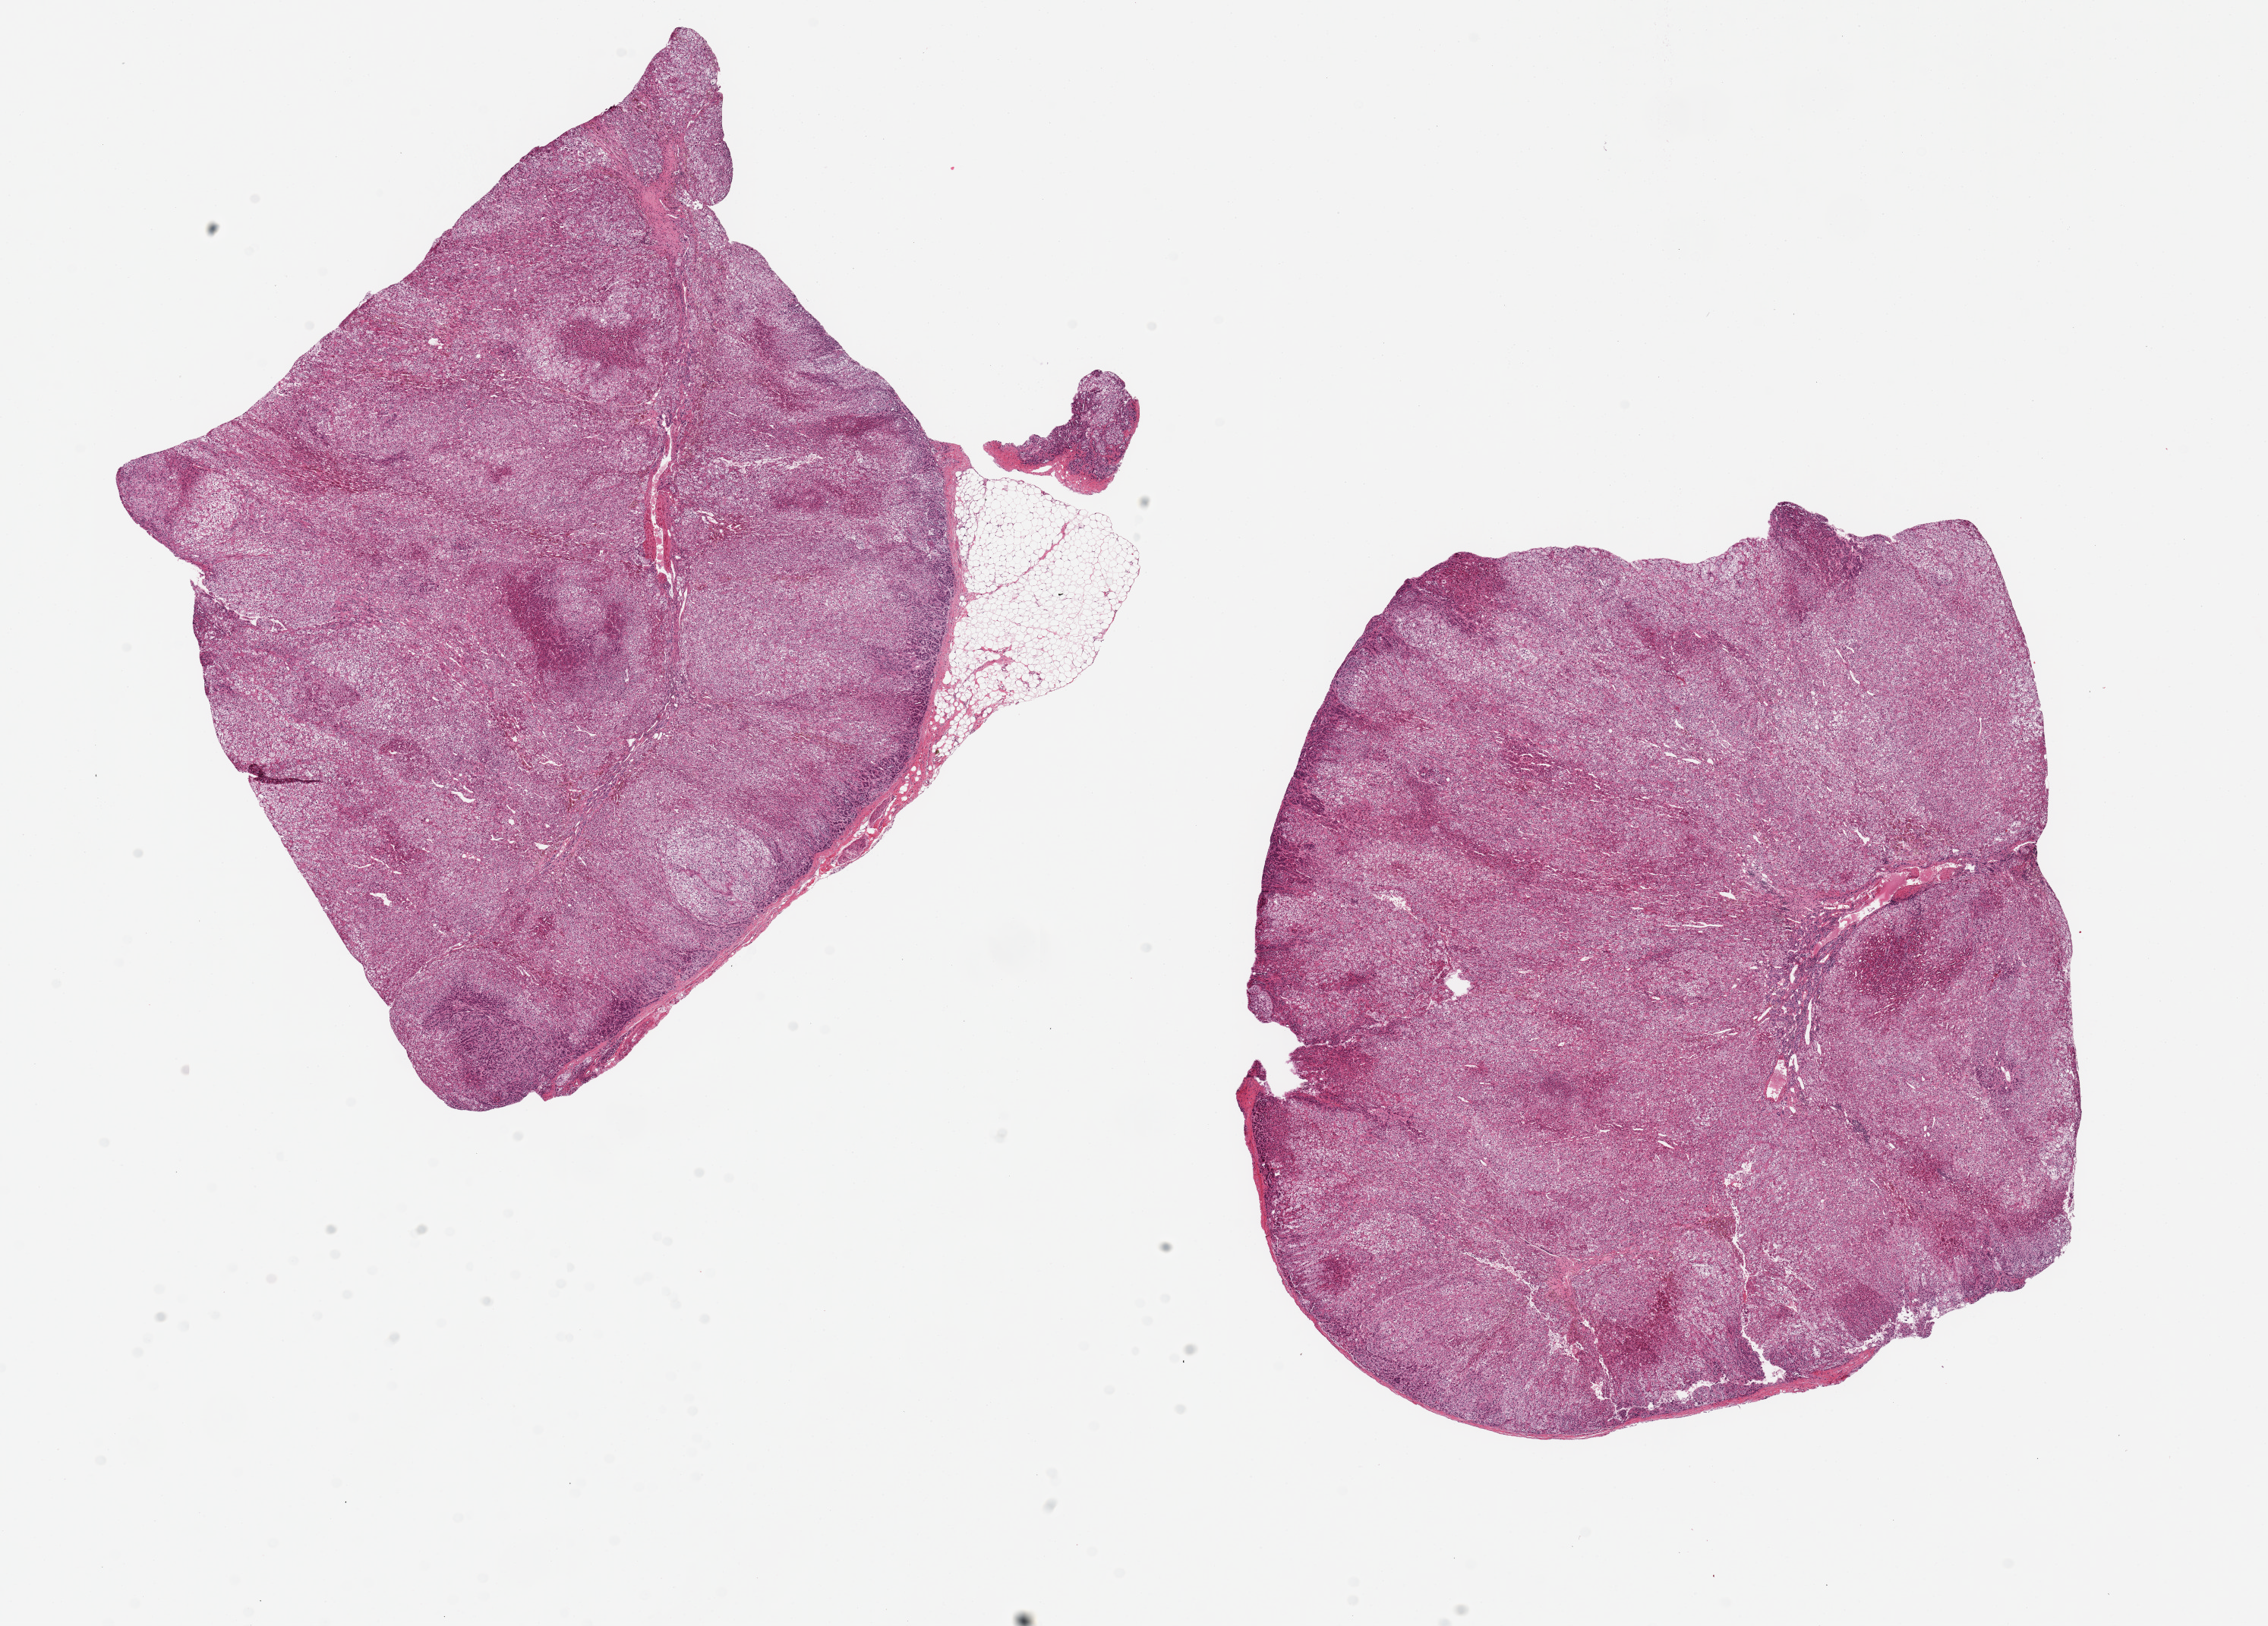
Hematoxylin and eosin (H&E) whole-slide image — a low-resolution overview of the entire scanned area, about 23.6 x 16.9 mm; PAXgene-fixed, paraffin-embedded tissue; sampled site (target tissue): adrenal gland; donor tissue sample.
Reviewer comment on this tissue sample: 2 pieces ~9x9mm, all cortex, reasonabley well preserved, minimal adherent fat.